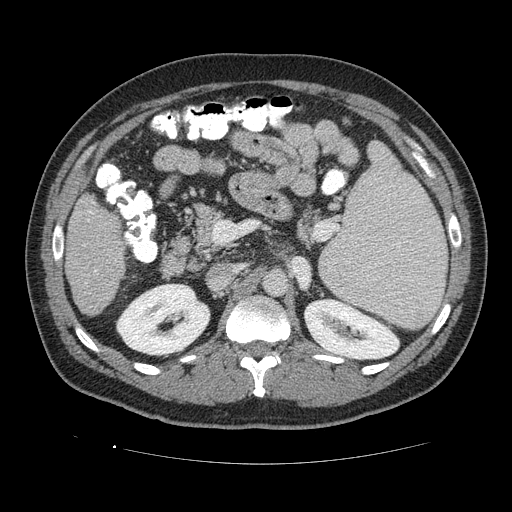
Contrast-enhanced abdominal CT (liver protocol), one axial slice. Slice 60 of 113 in the series (ordered by position). Reconstruction kernel STANDARD. Soft-tissue window (W 400 / L 40 HU). 512 × 512 image matrix, field of view 400 × 400 mm. From the clinical record (not read from this slice): diagnosis: hepatocellular carcinoma (patient treated with transarterial chemoembolisation; whether this scan precedes or follows treatment is not stated here); TNM stage (as recorded): Stage-II; Child-Pugh class: B; tumour differentiation: moderately differentiated; tumour nodularity: multinodular.
Outlined on this slice (semi-automatic segmentation, software-assisted and operator-edited):
- liver parenchyma outside the tumour (the mass and vessels are separate outlines, so this box may not span the whole liver): bounding box (x1, y1, x2, y2) in pixels: (64, 192, 130, 318)
- liver vessels: (87, 210, 95, 271)